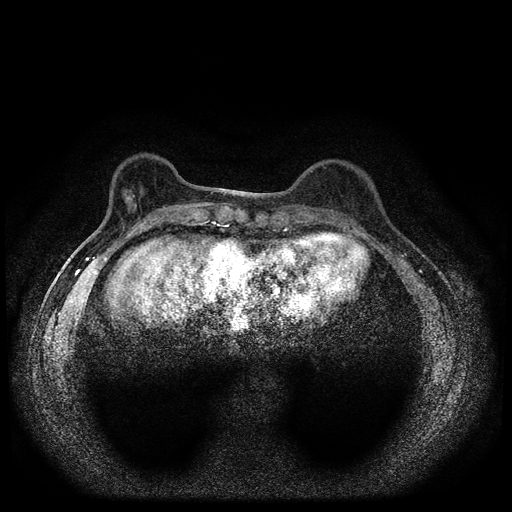
Breast MRI (dynamic contrast-enhanced, multi-phase), one axial slice. Position 27 of 112 along the scan axis. Dynamic contrast-enhanced series, time point 2 of 5 at this slice position (early post-contrast). 1.5 T. TE 2.7 ms, TR 5.4 ms. 2 mm slice thickness. 512 × 512 image matrix, field of view 320 × 320 mm. Patient: female, 61 years.
Structures marked on this image (semi-automatic segmentation, software-assisted and operator-edited):
- breast lesion (labelled benign in the annotation): box from (x=123, y=189) to (x=135, y=202) px